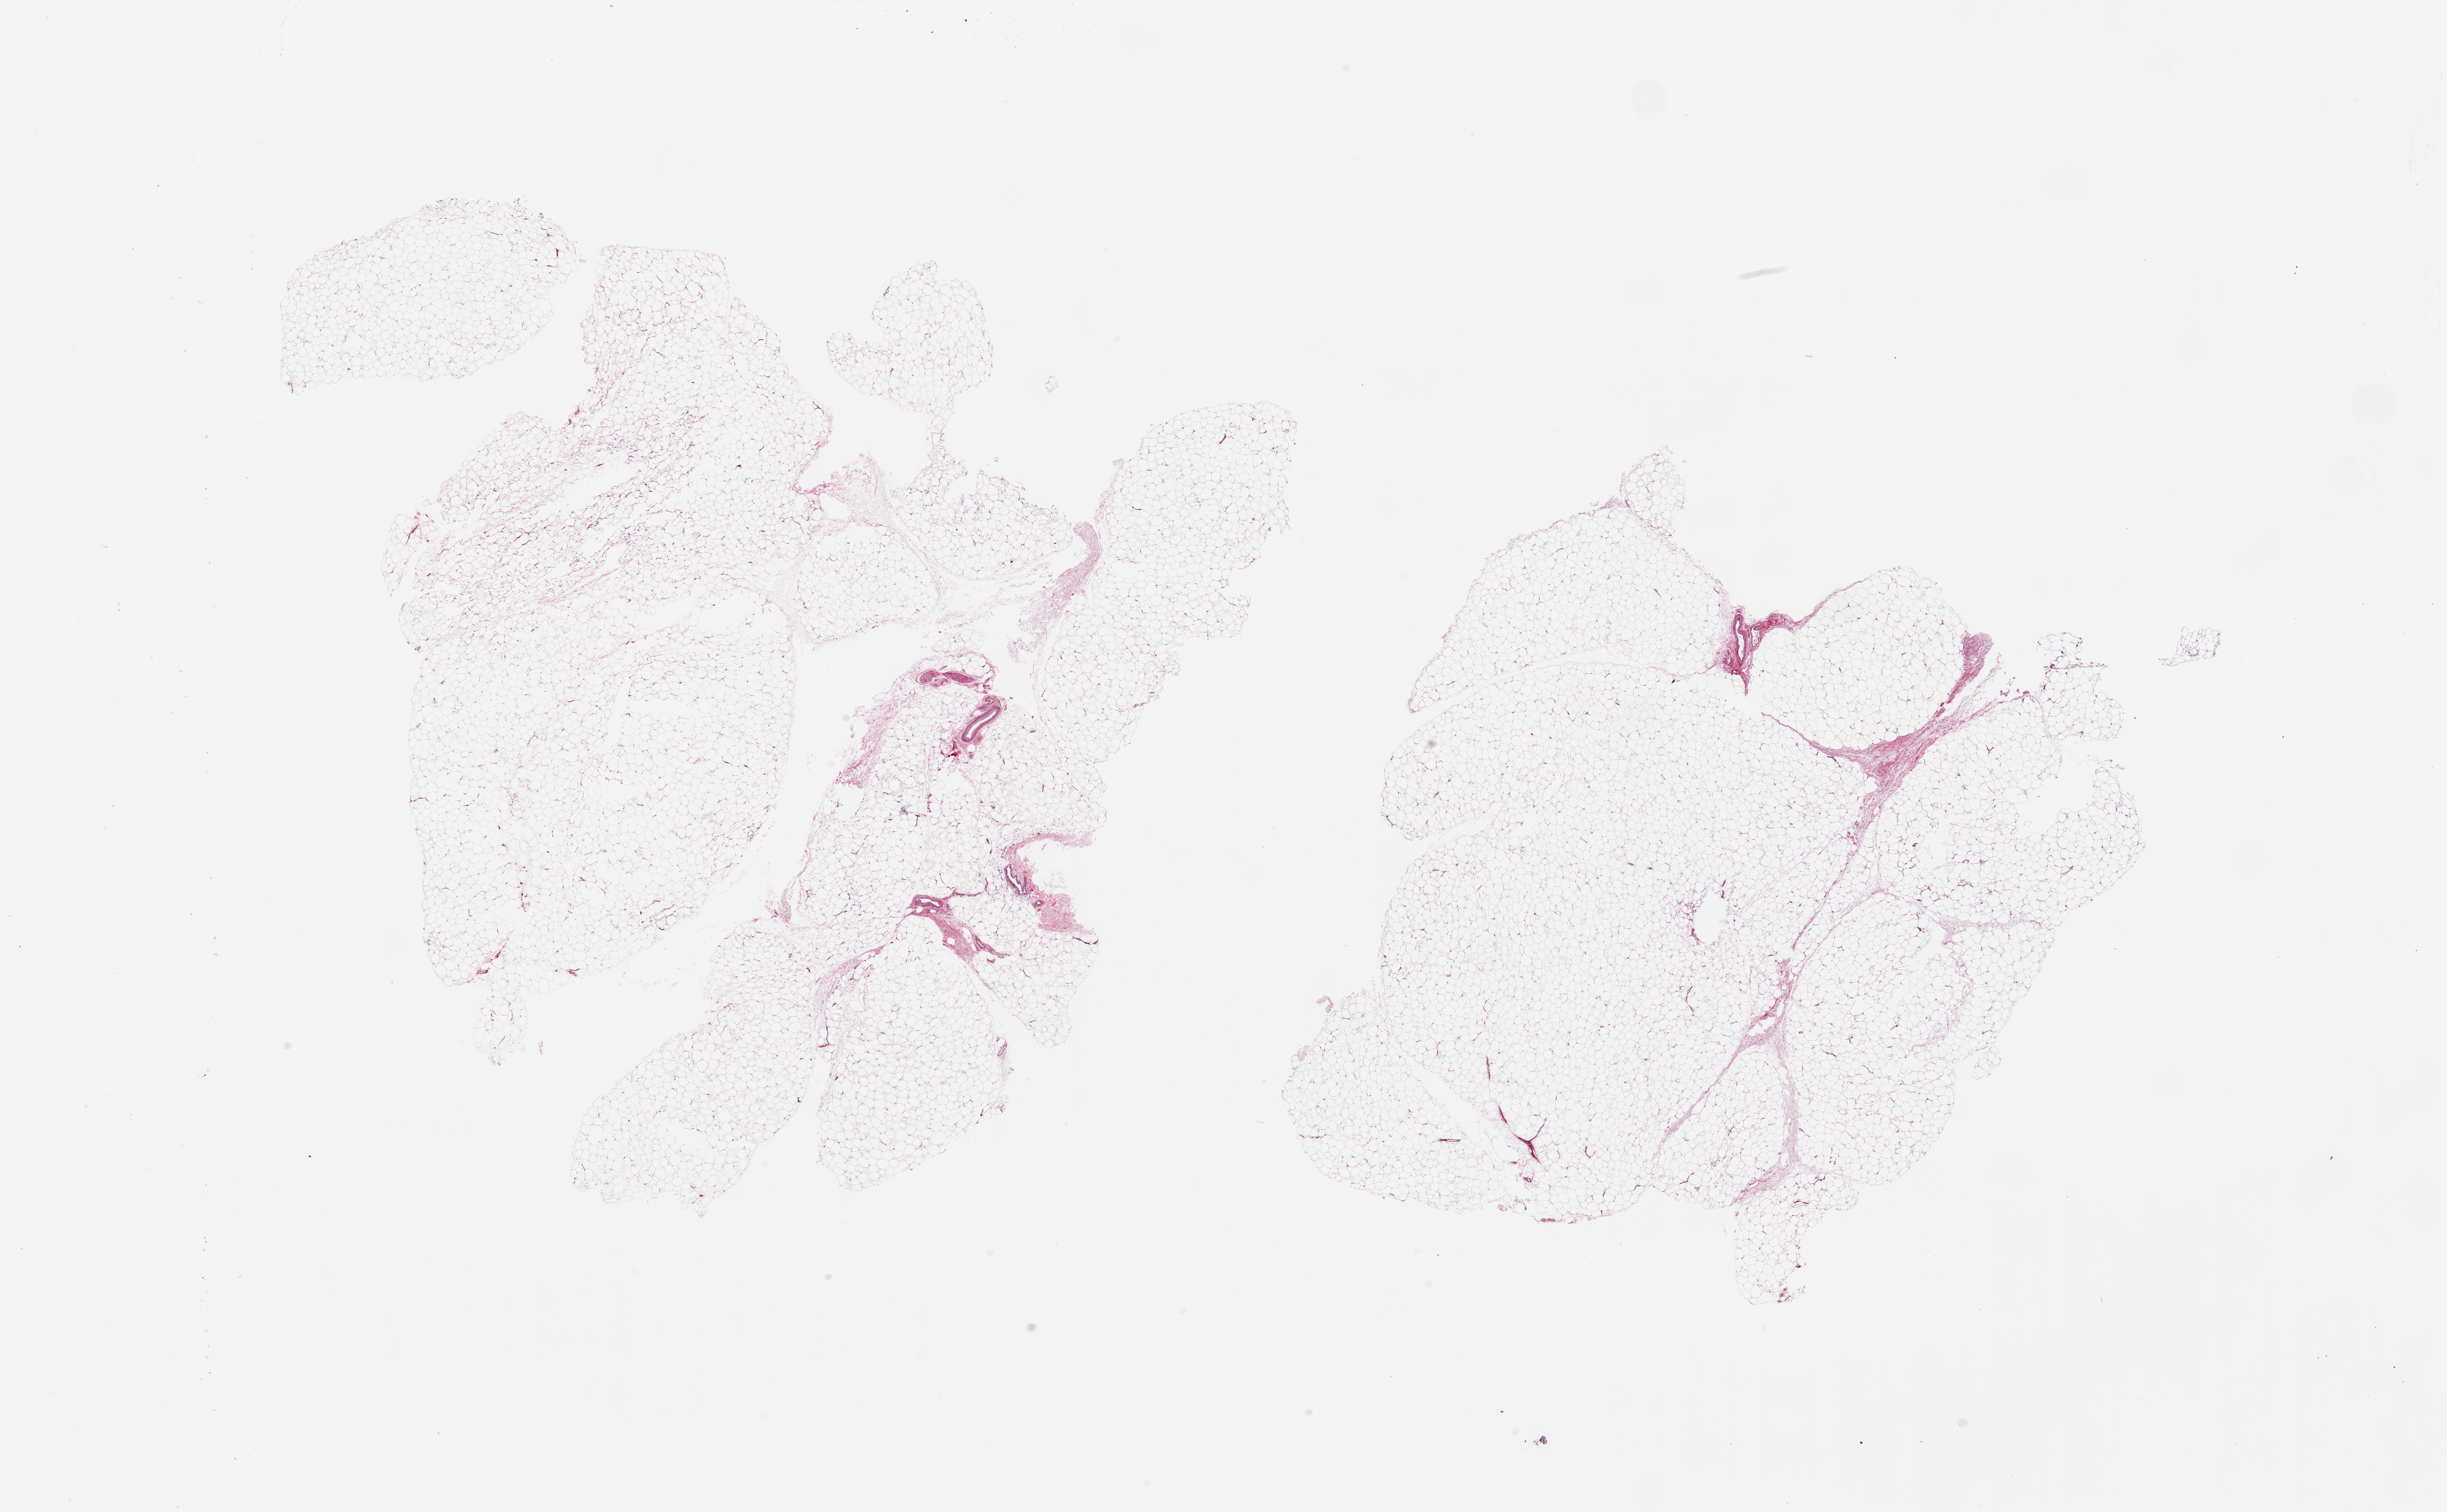
Whole-slide image, haematoxylin and eosin stain, brightfield — whole scanned area (about 31.5 x 19.5 mm, acquisition: 20x scan) shown as a low-resolution overview. PAXgene-fixed paraffin-embedded (PFPE) section. Sampled site (target tissue): adipose tissue. Tissue donor sample. Female donor.
- review note (as recorded): 2 piece, <5% vascular elements